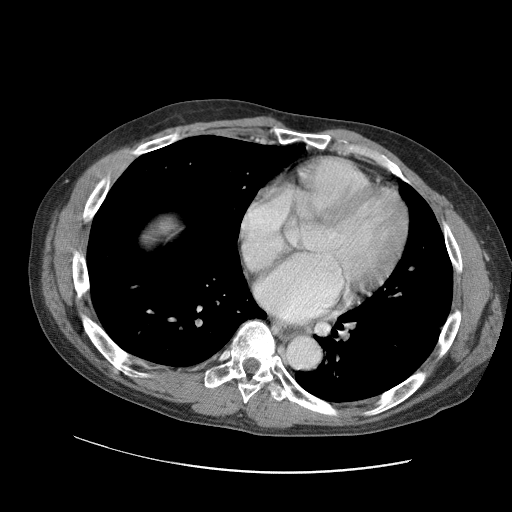
Contrast-enhanced abdominal CT (liver protocol), one axial slice; position 100 of 109 along the scan axis; soft-tissue window (W 400 / L 40 HU); 512 × 512 image matrix. From the clinical record (not read from this slice): diagnosis: hepatocellular carcinoma (patient treated with transarterial chemoembolisation; whether this scan precedes or follows treatment is not stated here); TNM stage (as recorded): Stage-IIIC; Child-Pugh class: B.
Outlined on this slice (semi-automatically segmented with operator editing):
- liver parenchyma outside the tumour (the mass and vessels are separate outlines, so this box may not span the whole liver): box from (x=152, y=216) to (x=178, y=236) px